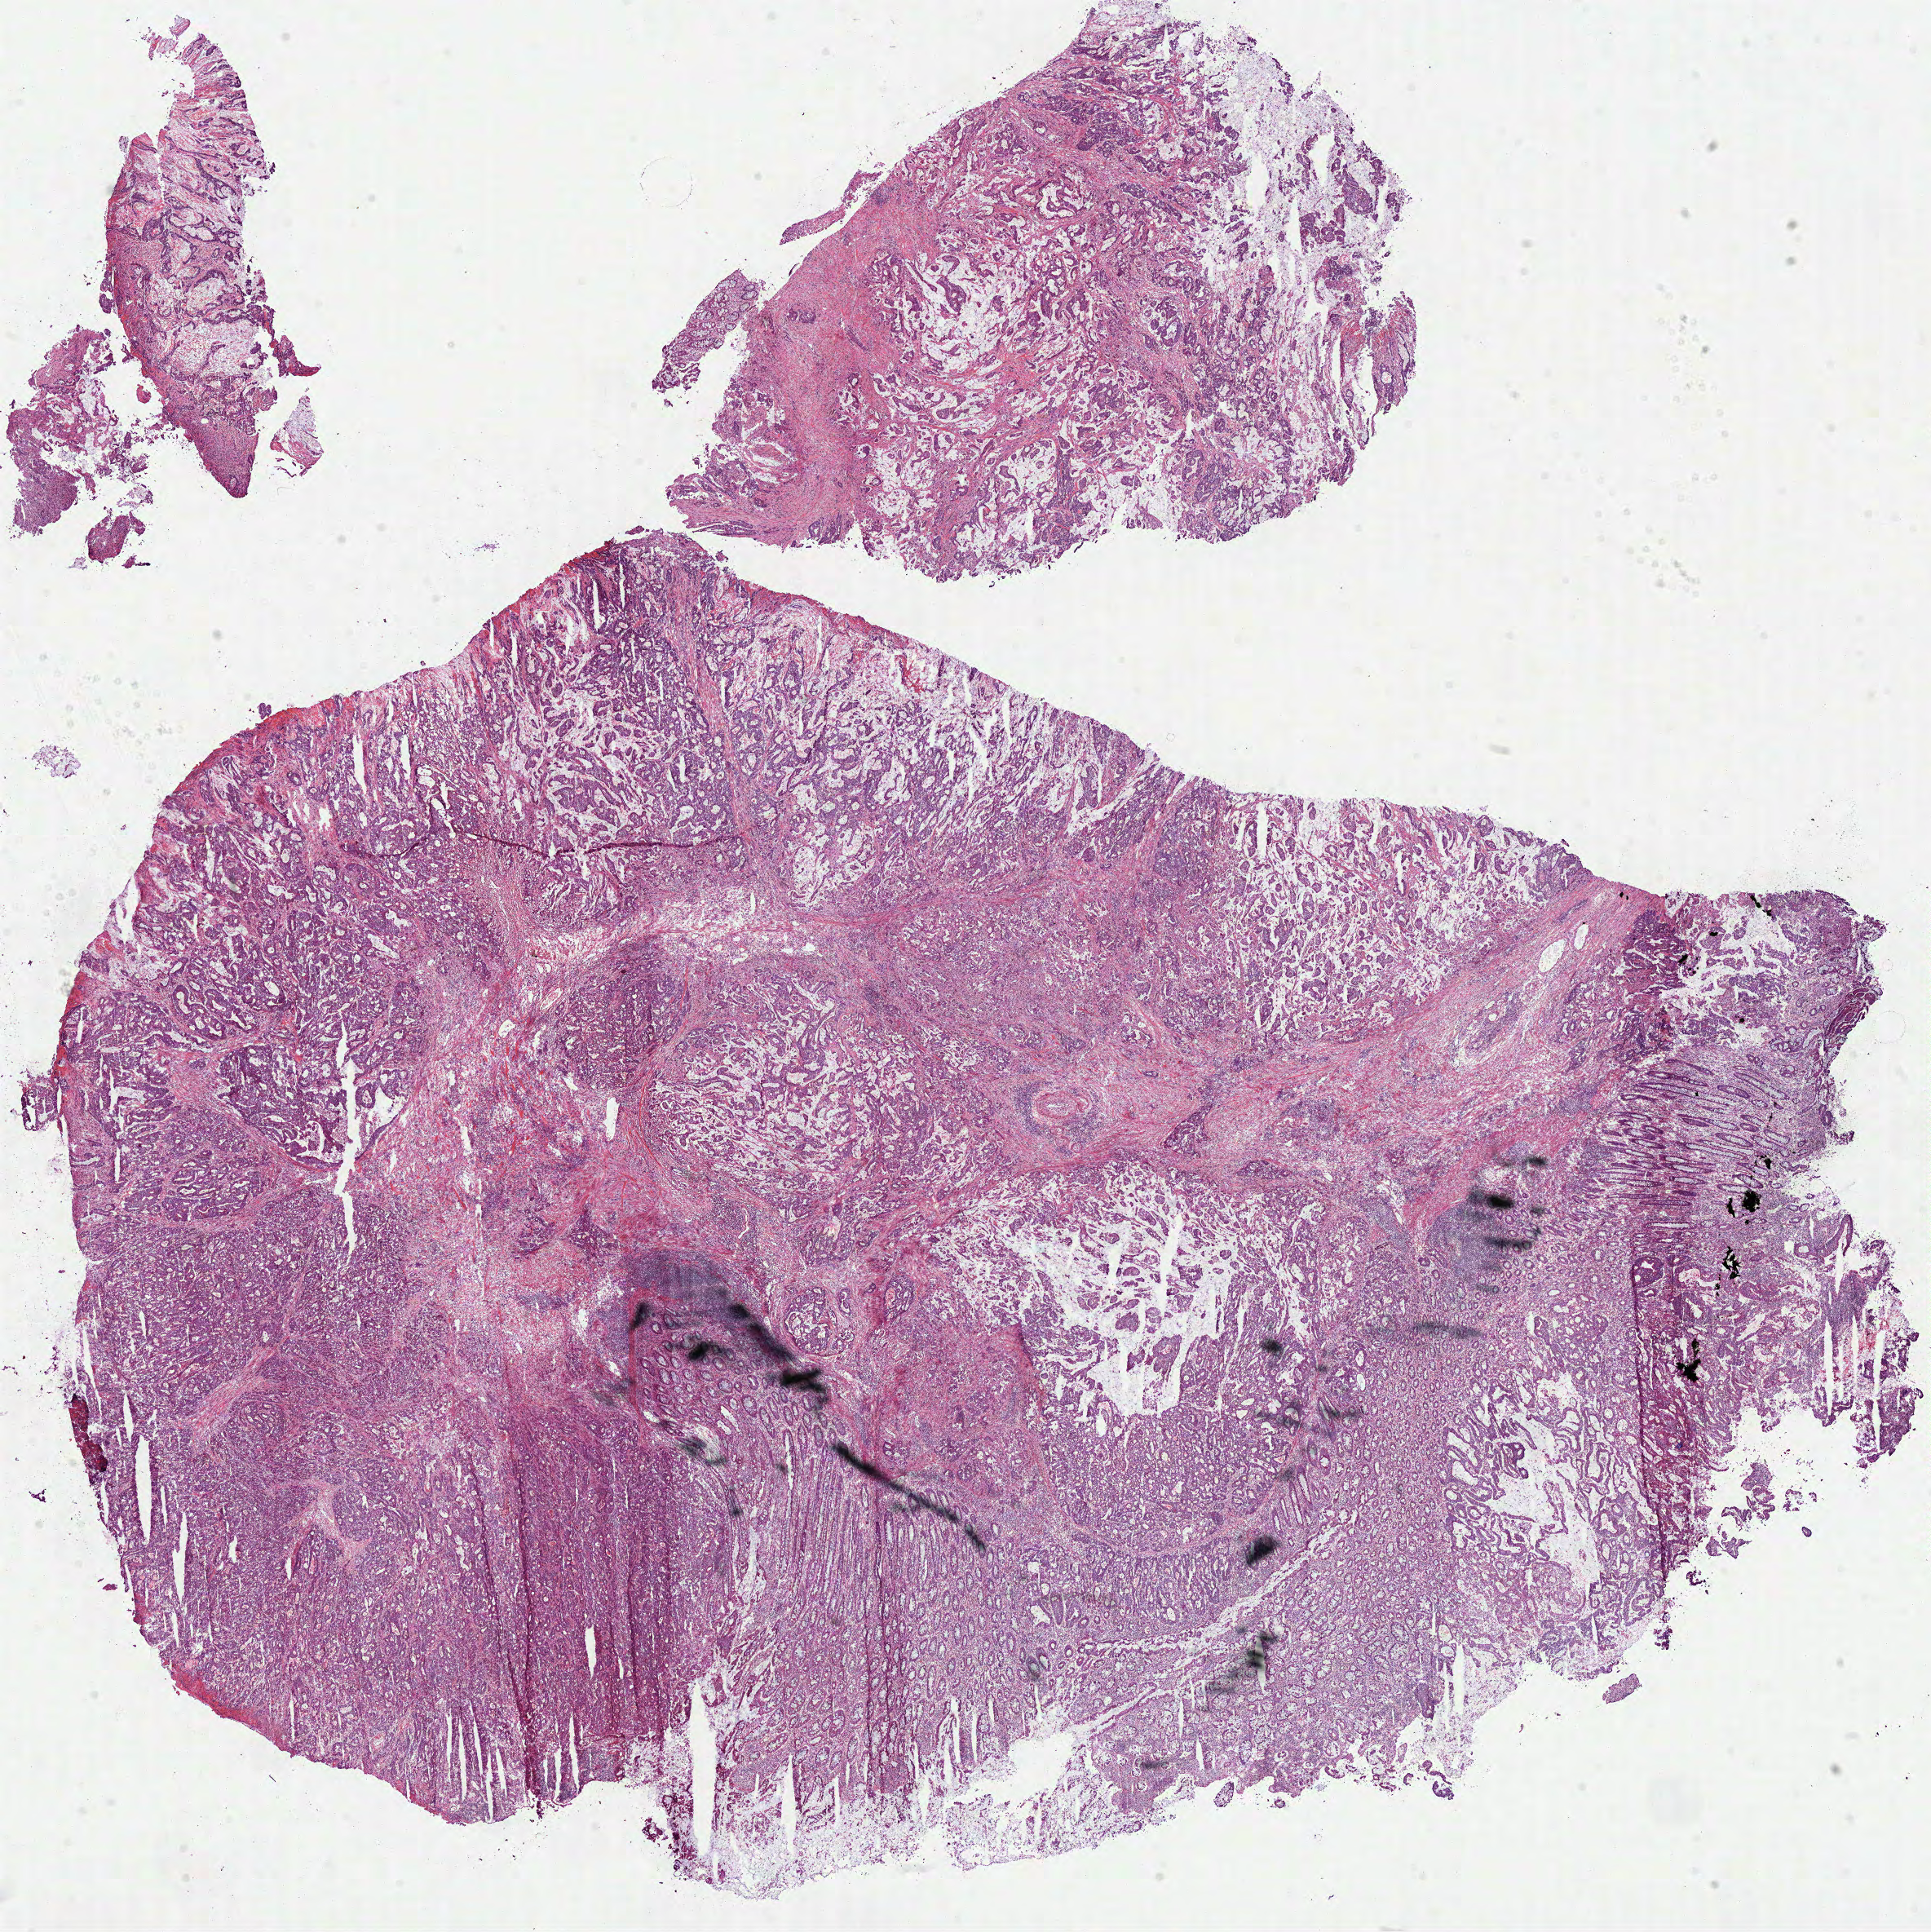
Digitized Hematoxylin and eosin (H&E) stained tissue section (whole slide), whole scanned area (about 19.1 x 19.1 mm) shown as a low-resolution overview. Frozen section from the top of the tissue portion. Sample: primary tumour, colon. Male patient; age at initial diagnosis 64 years. Pathologist review of this section (percent, as recorded): tumour cells 55%, tumour nuclei 75%, normal cells 20%, stromal cells 20%, necrosis 5%.
- pathologic diagnosis: Adenocarcinoma, NOS (ascending colon)
- AJCC pathologic stage: IV (5th edition)
- lymph nodes positive (case pathology): 1 of 10 examined